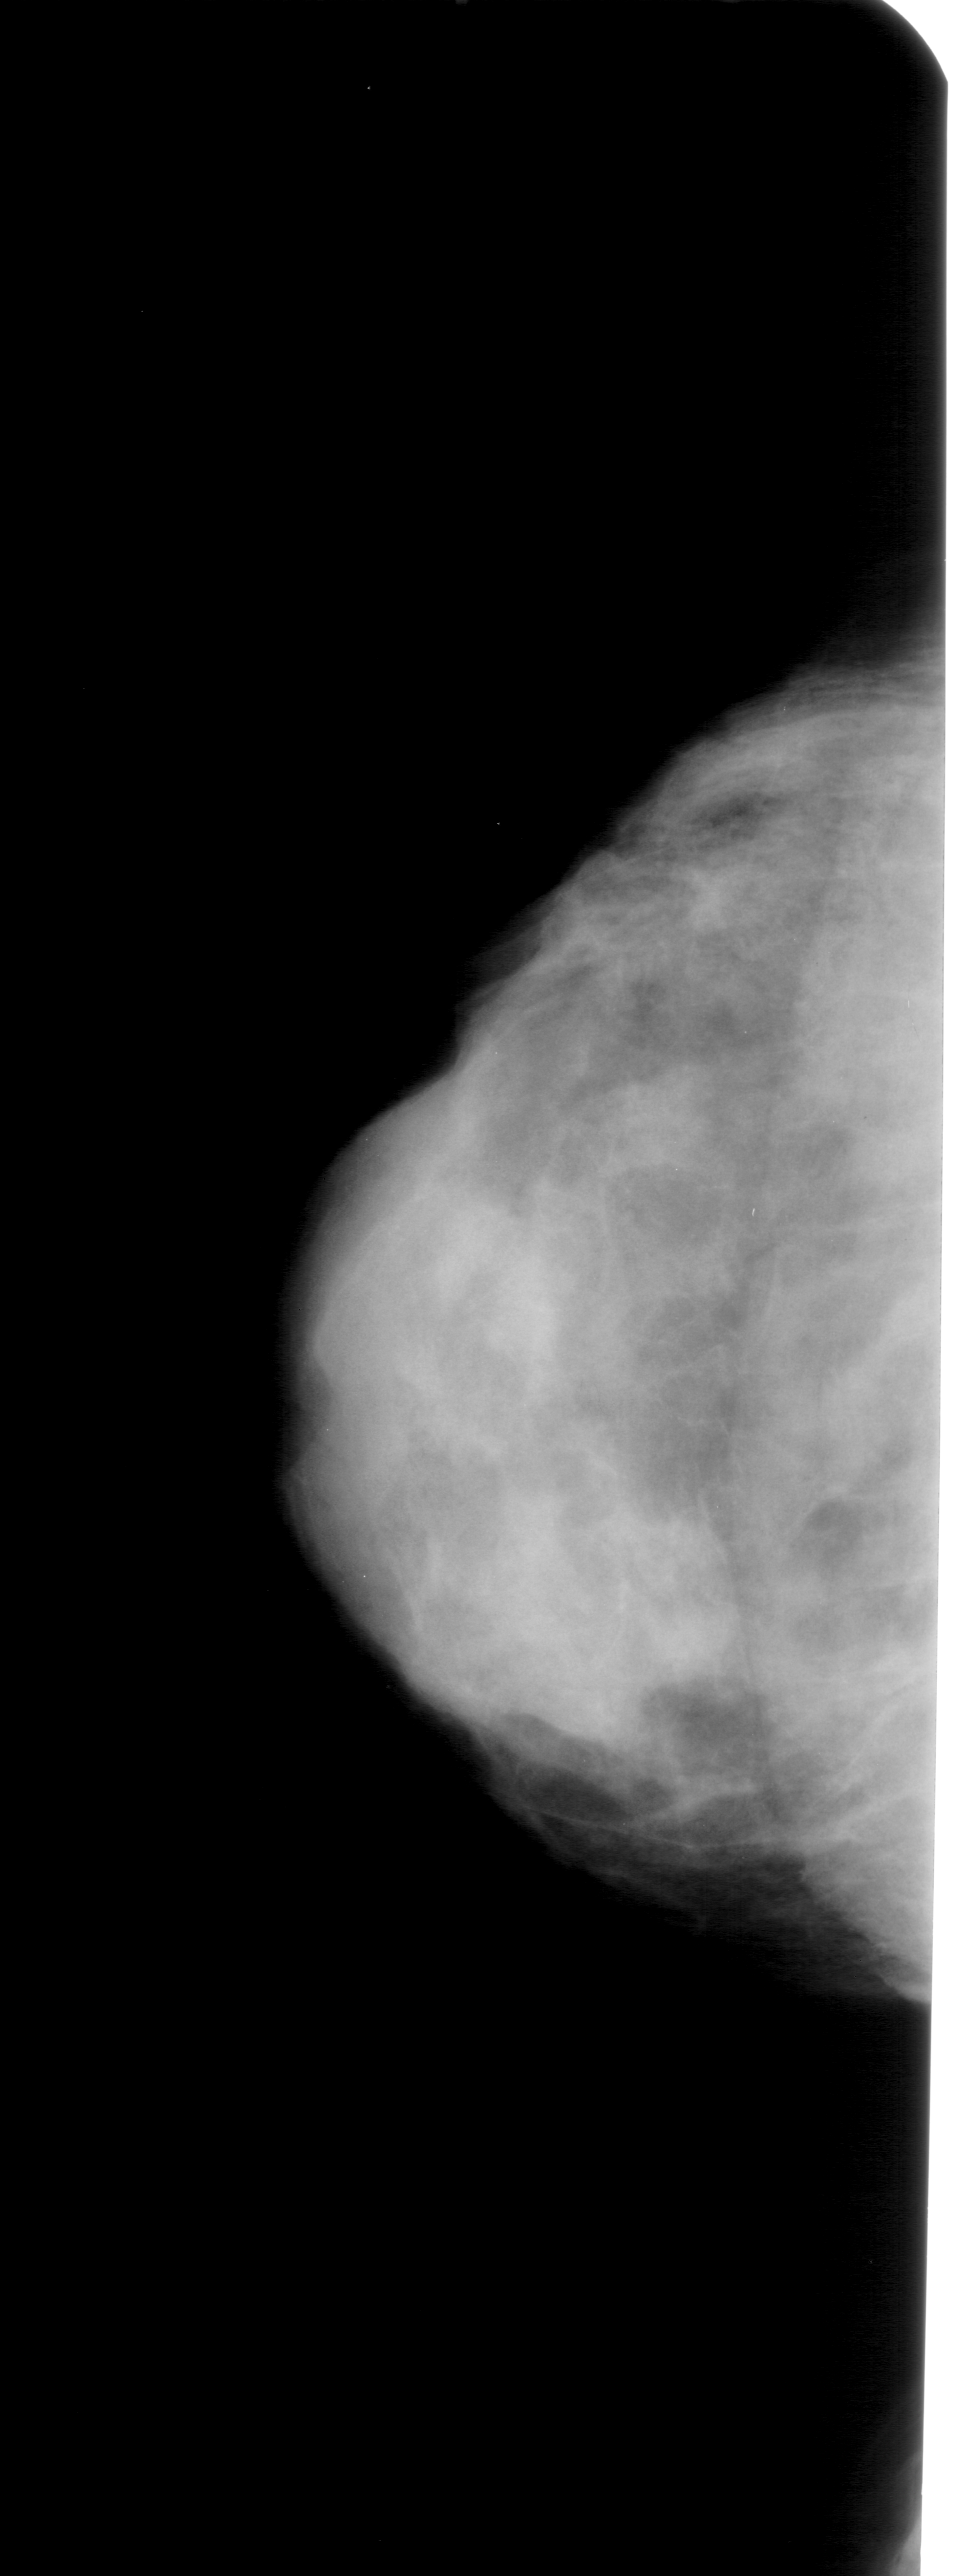
Scanned film-screen mammogram; left breast; craniocaudal (CC) view; breast composition: extremely dense (BI-RADS density category 4 of 4); 953 × 2576 image matrix.
Marked abnormalities (boxes around the expert regions of interest):
- calcifications, morphology pleomorphic, distribution clustered; BI-RADS assessment category 4; pathology (as recorded): benign: bounding box (x1, y1, x2, y2) in pixels: (368, 1170, 445, 1258)